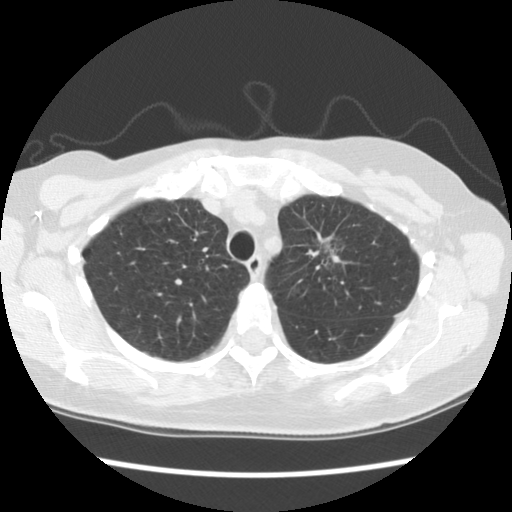
Chest CT (low-dose screening protocol), one axial image; second screening round (one year after baseline); lung window (W 1500 / L -600 HU). Female participant, aged 65 years at enrolment. Former smoker at enrolment.
Lesion marked by an expert reader, bounding box <301,224,363,285> (left, top, right, bottom; pixels). The screening reader recorded 2 non-calcified nodules or masses ≥4 mm on this exam; which of them this box marks is not recorded. Participant outcome: lung cancer diagnosed 481 days after this screen — adenocarcinoma, NOS, left upper lobe, moderately differentiated (G2), stage IA (AJCC 6th edition), 30 mm at pathology.